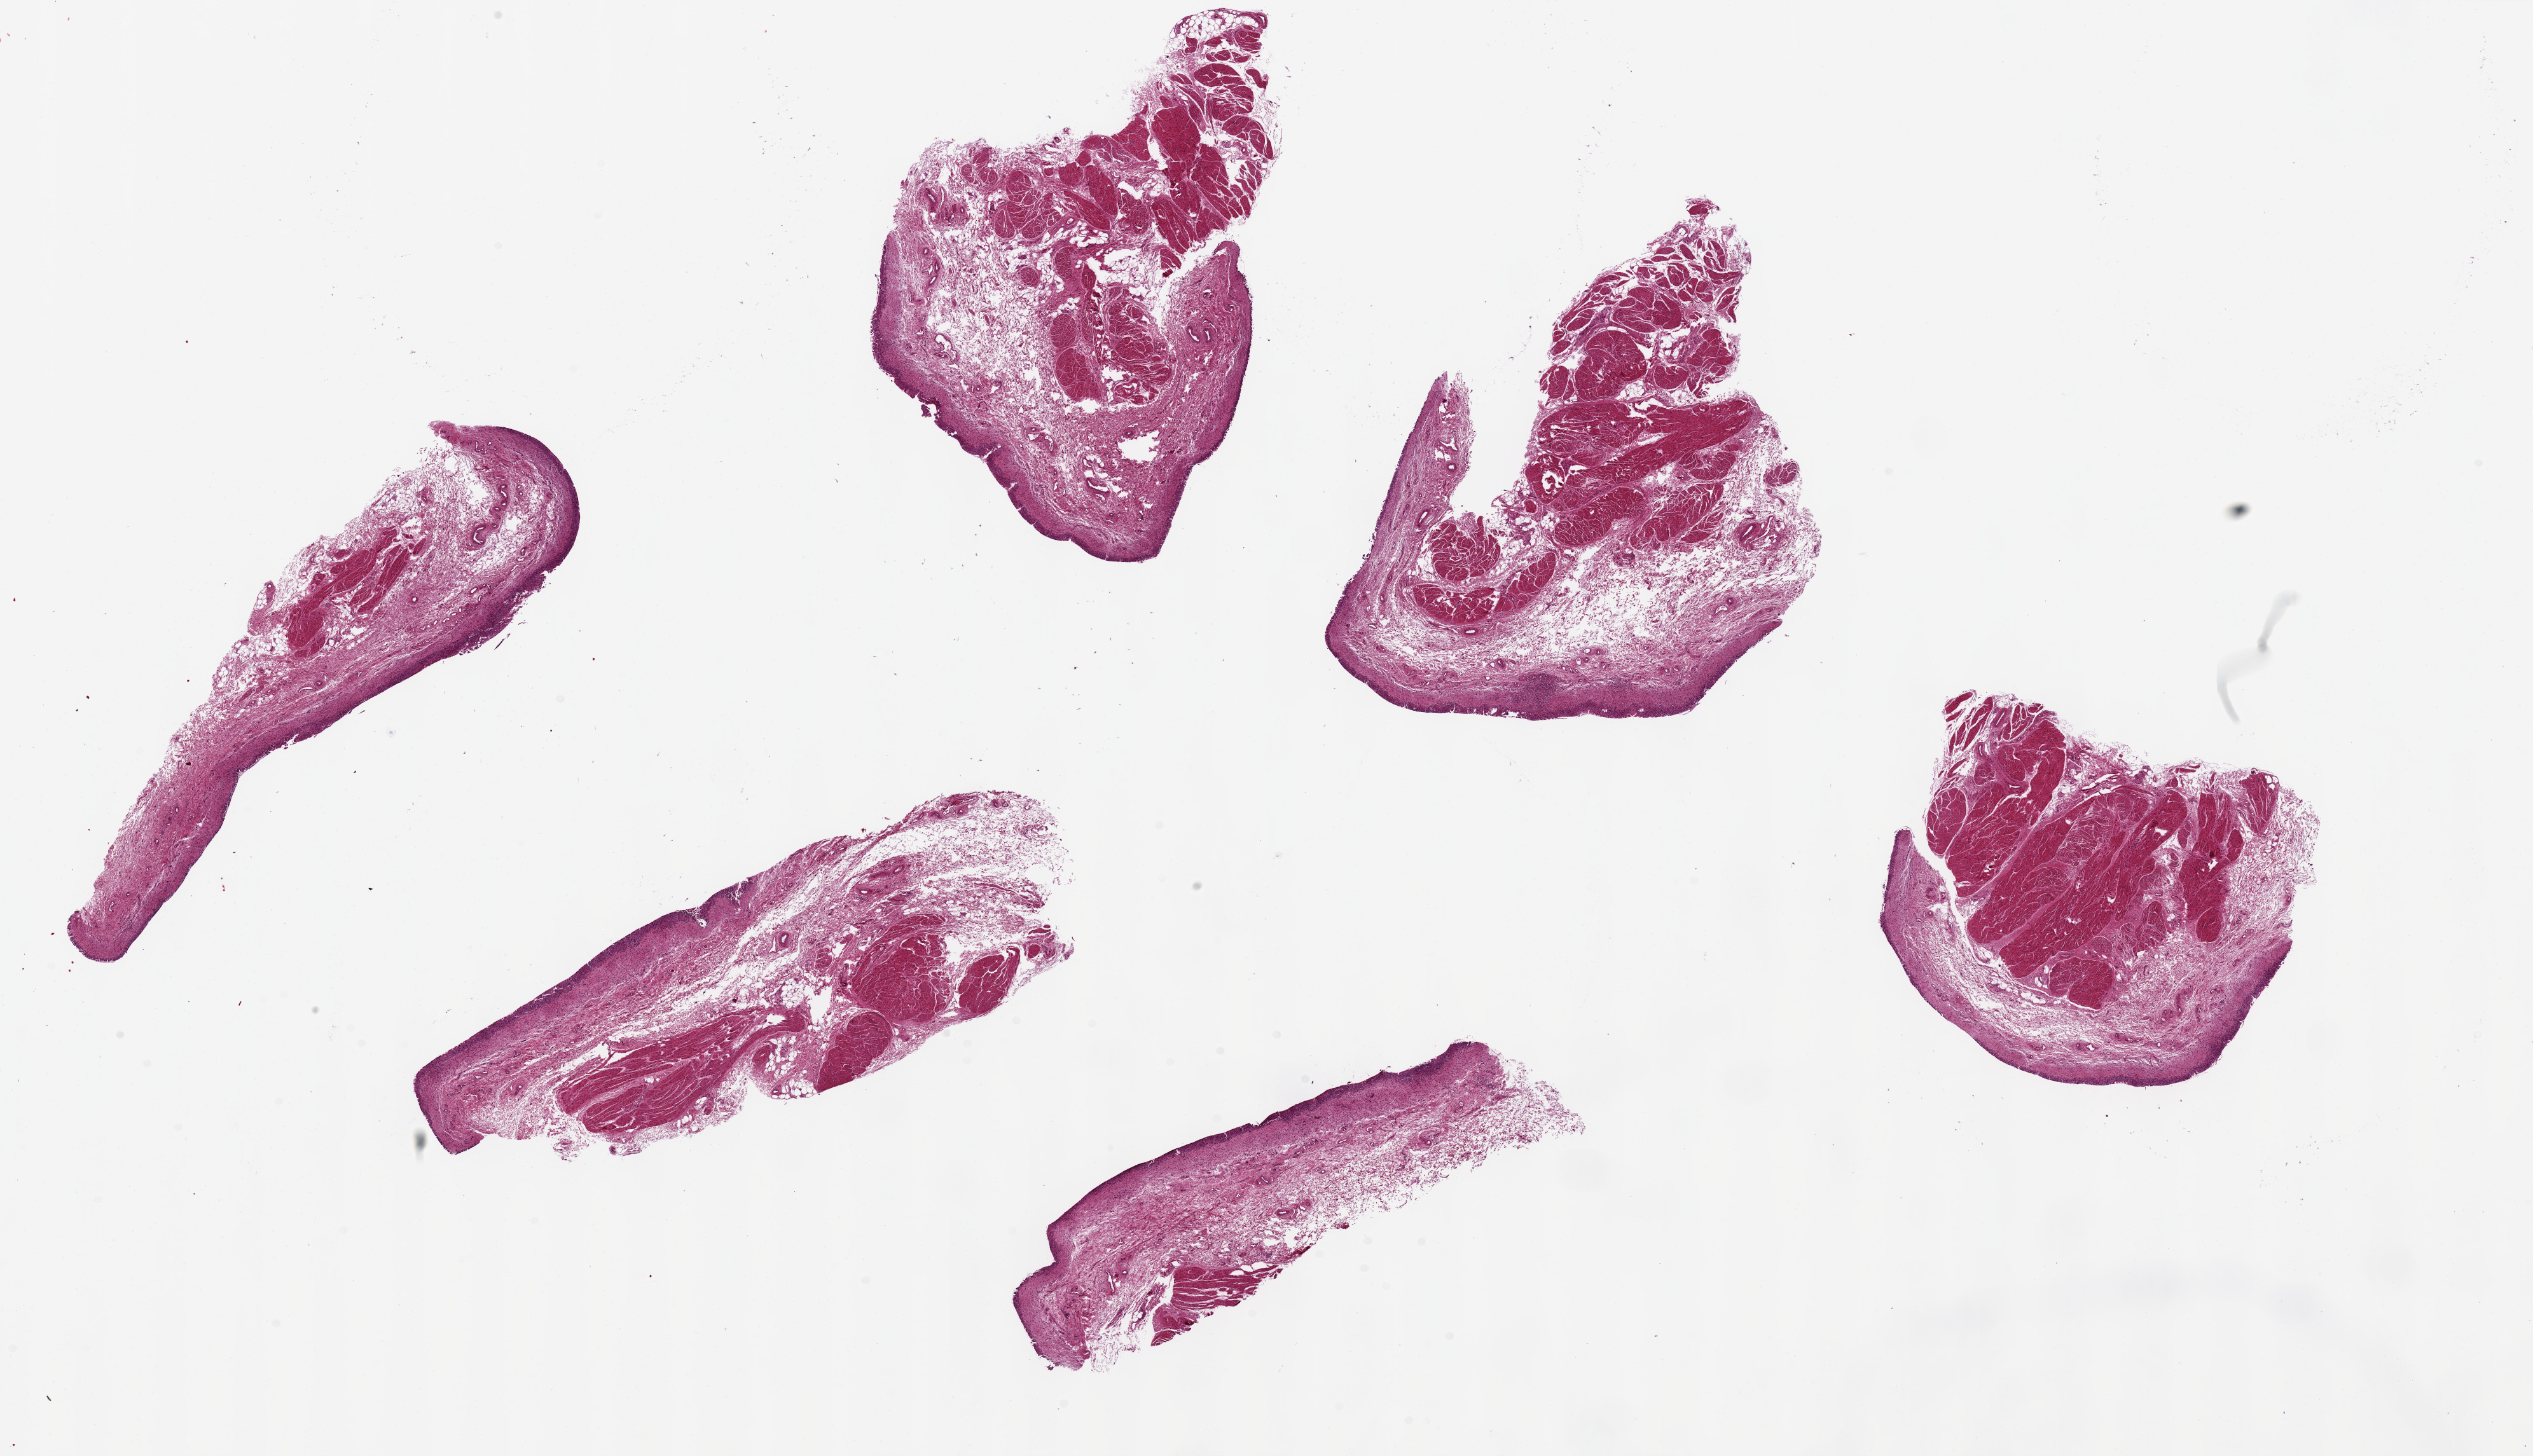
Haematoxylin and eosin whole-slide image — whole scanned area (about 31.5 x 18.1 mm, acquisition: 20x scan) shown as a low-resolution overview, PAXgene-fixed, paraffin-embedded tissue, sampled site (target tissue): urinary bladder, donor tissue sample. Donor sex: female.
Pathologist's review note for this sample: 6 pieces, ~5 x 7mm, mucosa partly sloughed.